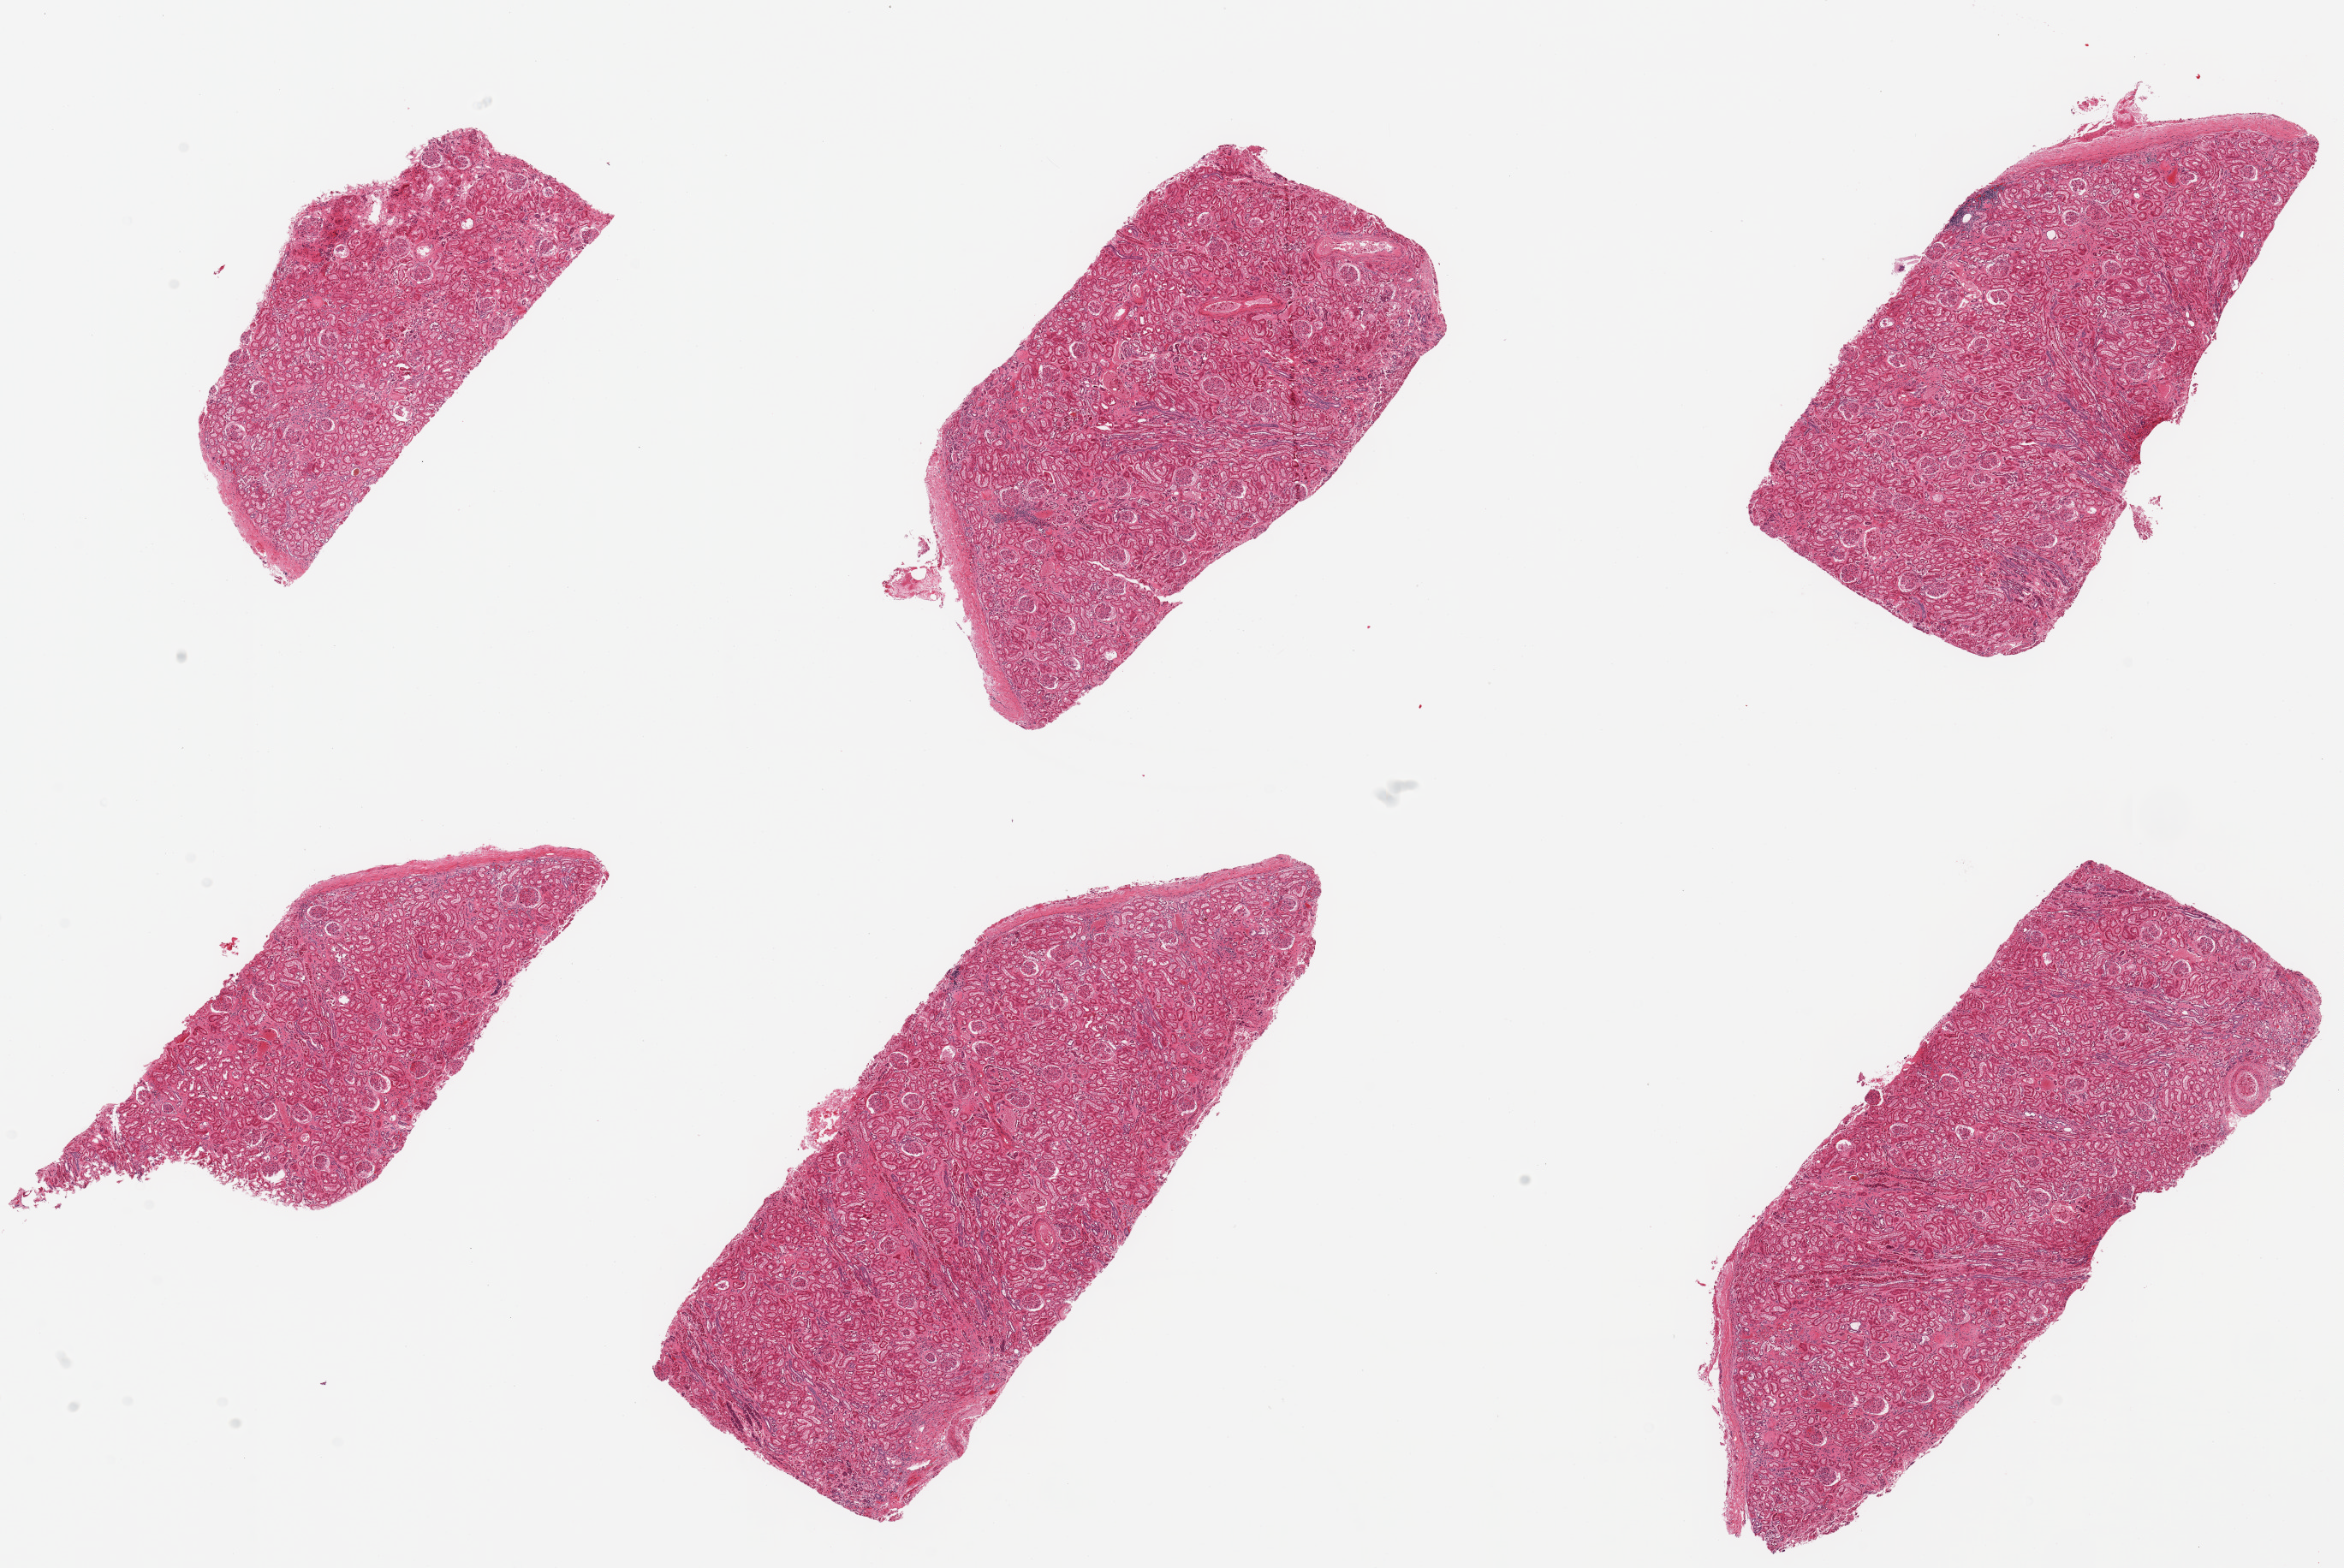
Hematoxylin and eosin (H&E) whole-slide image, low-resolution overview of the scanned area, about 21.7 x 14.5 mm (from a 20x scan); PAXgene-fixed, paraffin-embedded tissue; sampled site (target tissue): renal cortex; tissue donor sample. Donor: female.
Review note (as recorded): 6 pieces; no lesions.